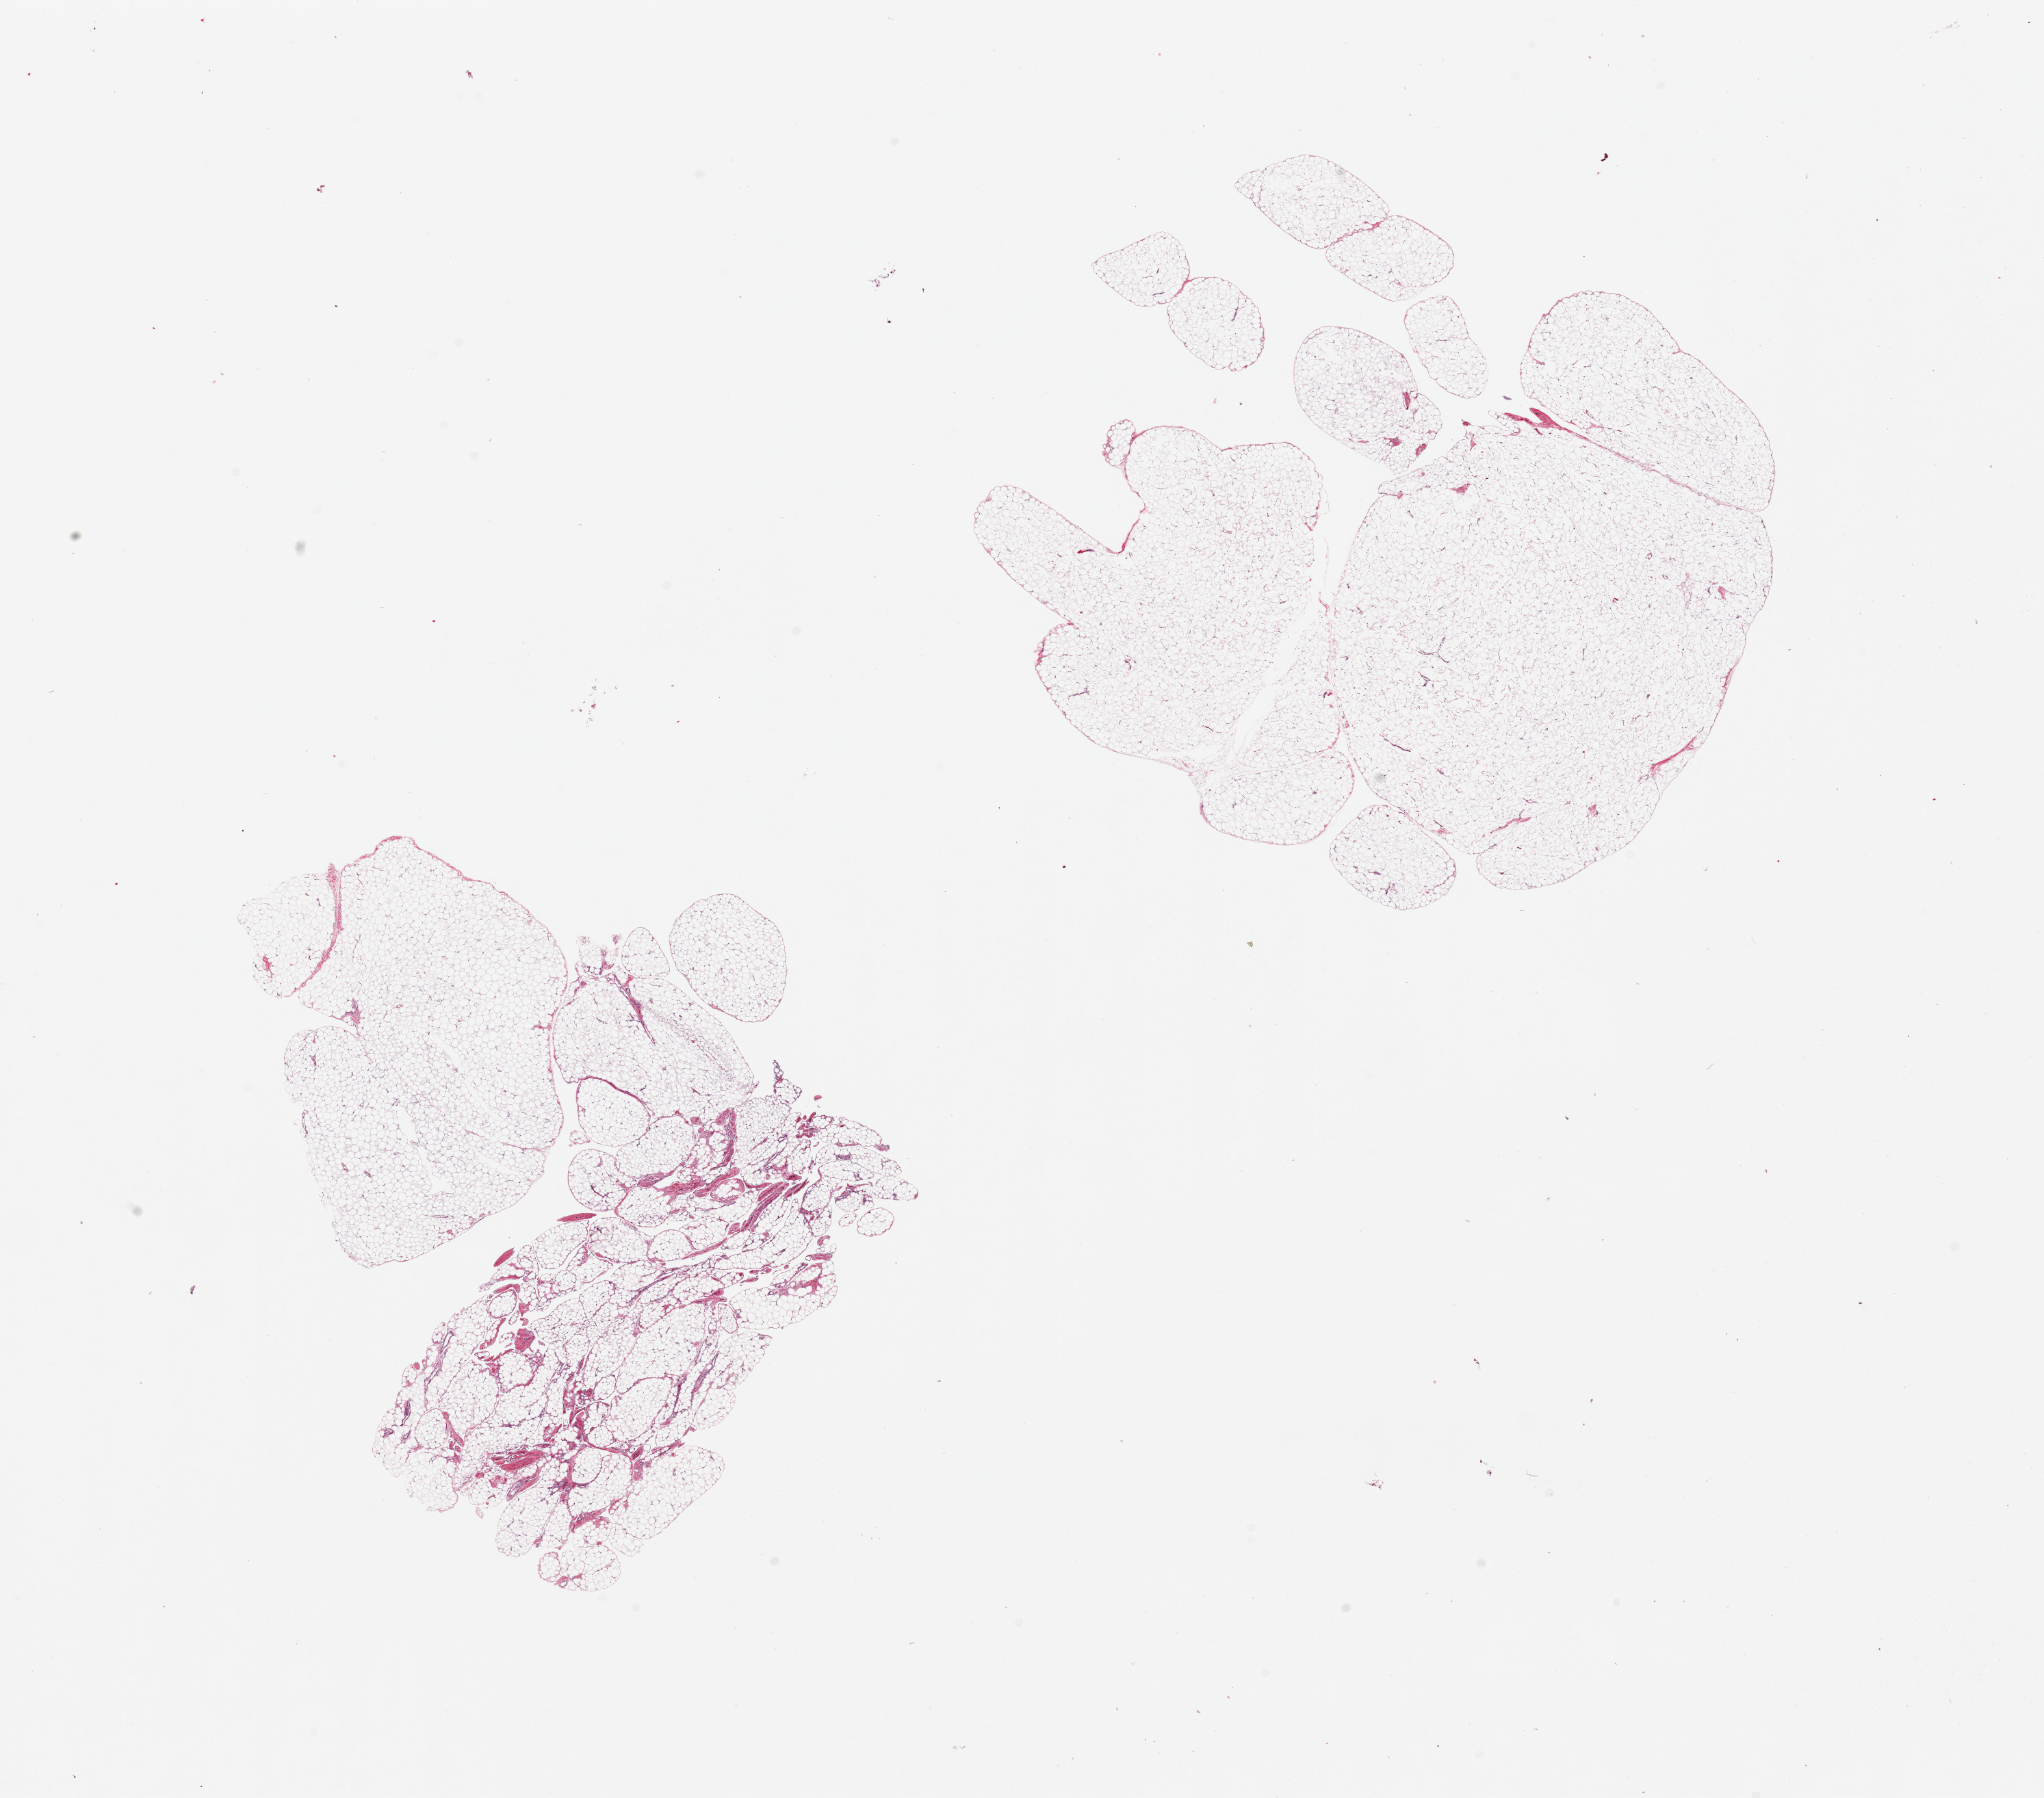
Whole-slide image, haematoxylin and eosin stain, a low-resolution overview of the entire scanned area, about 23.6 x 20.8 mm. PAXgene-fixed, paraffin-embedded tissue. Target tissue: omentum. Tissue donor sample.
Reviewer comment on this tissue sample: 2 pieces, one with prominent vessels, mesothelial reaction; aresa.